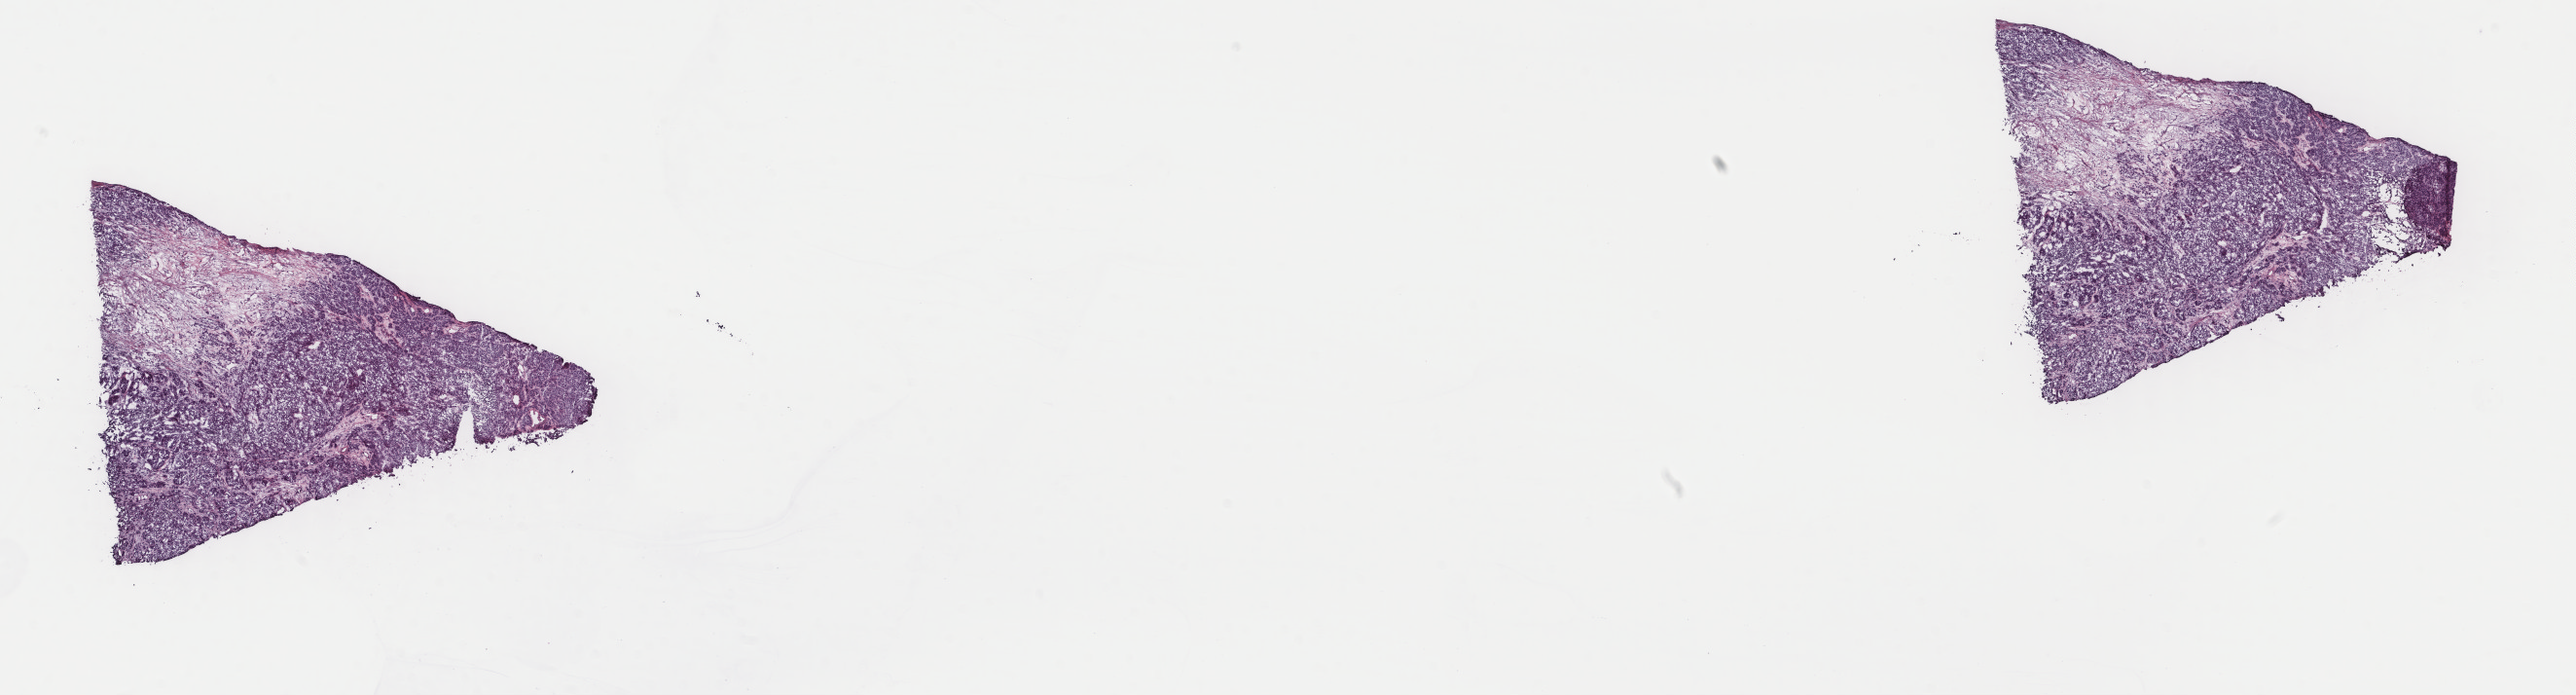
H&E-stained whole-slide image — whole scanned area (about 21.0 x 5.7 mm, slide scanned at 40x) shown as a low-resolution overview; frozen section; metastatic tumour sample, sampled site not recorded. Patient: male, age at initial diagnosis 58 years. Composition of this section per pathologist review: tumour cells 100%, tumour nuclei 85%, normal cells 0%, stromal cells 0%, necrosis 0%. Infiltration values recorded for this section: lymphocyte infiltration 0%, monocyte infiltration 0%, neutrophil infiltration 0%.
- this section: metastatic tumour tissue
- patient diagnosis: Malignant melanoma, NOS